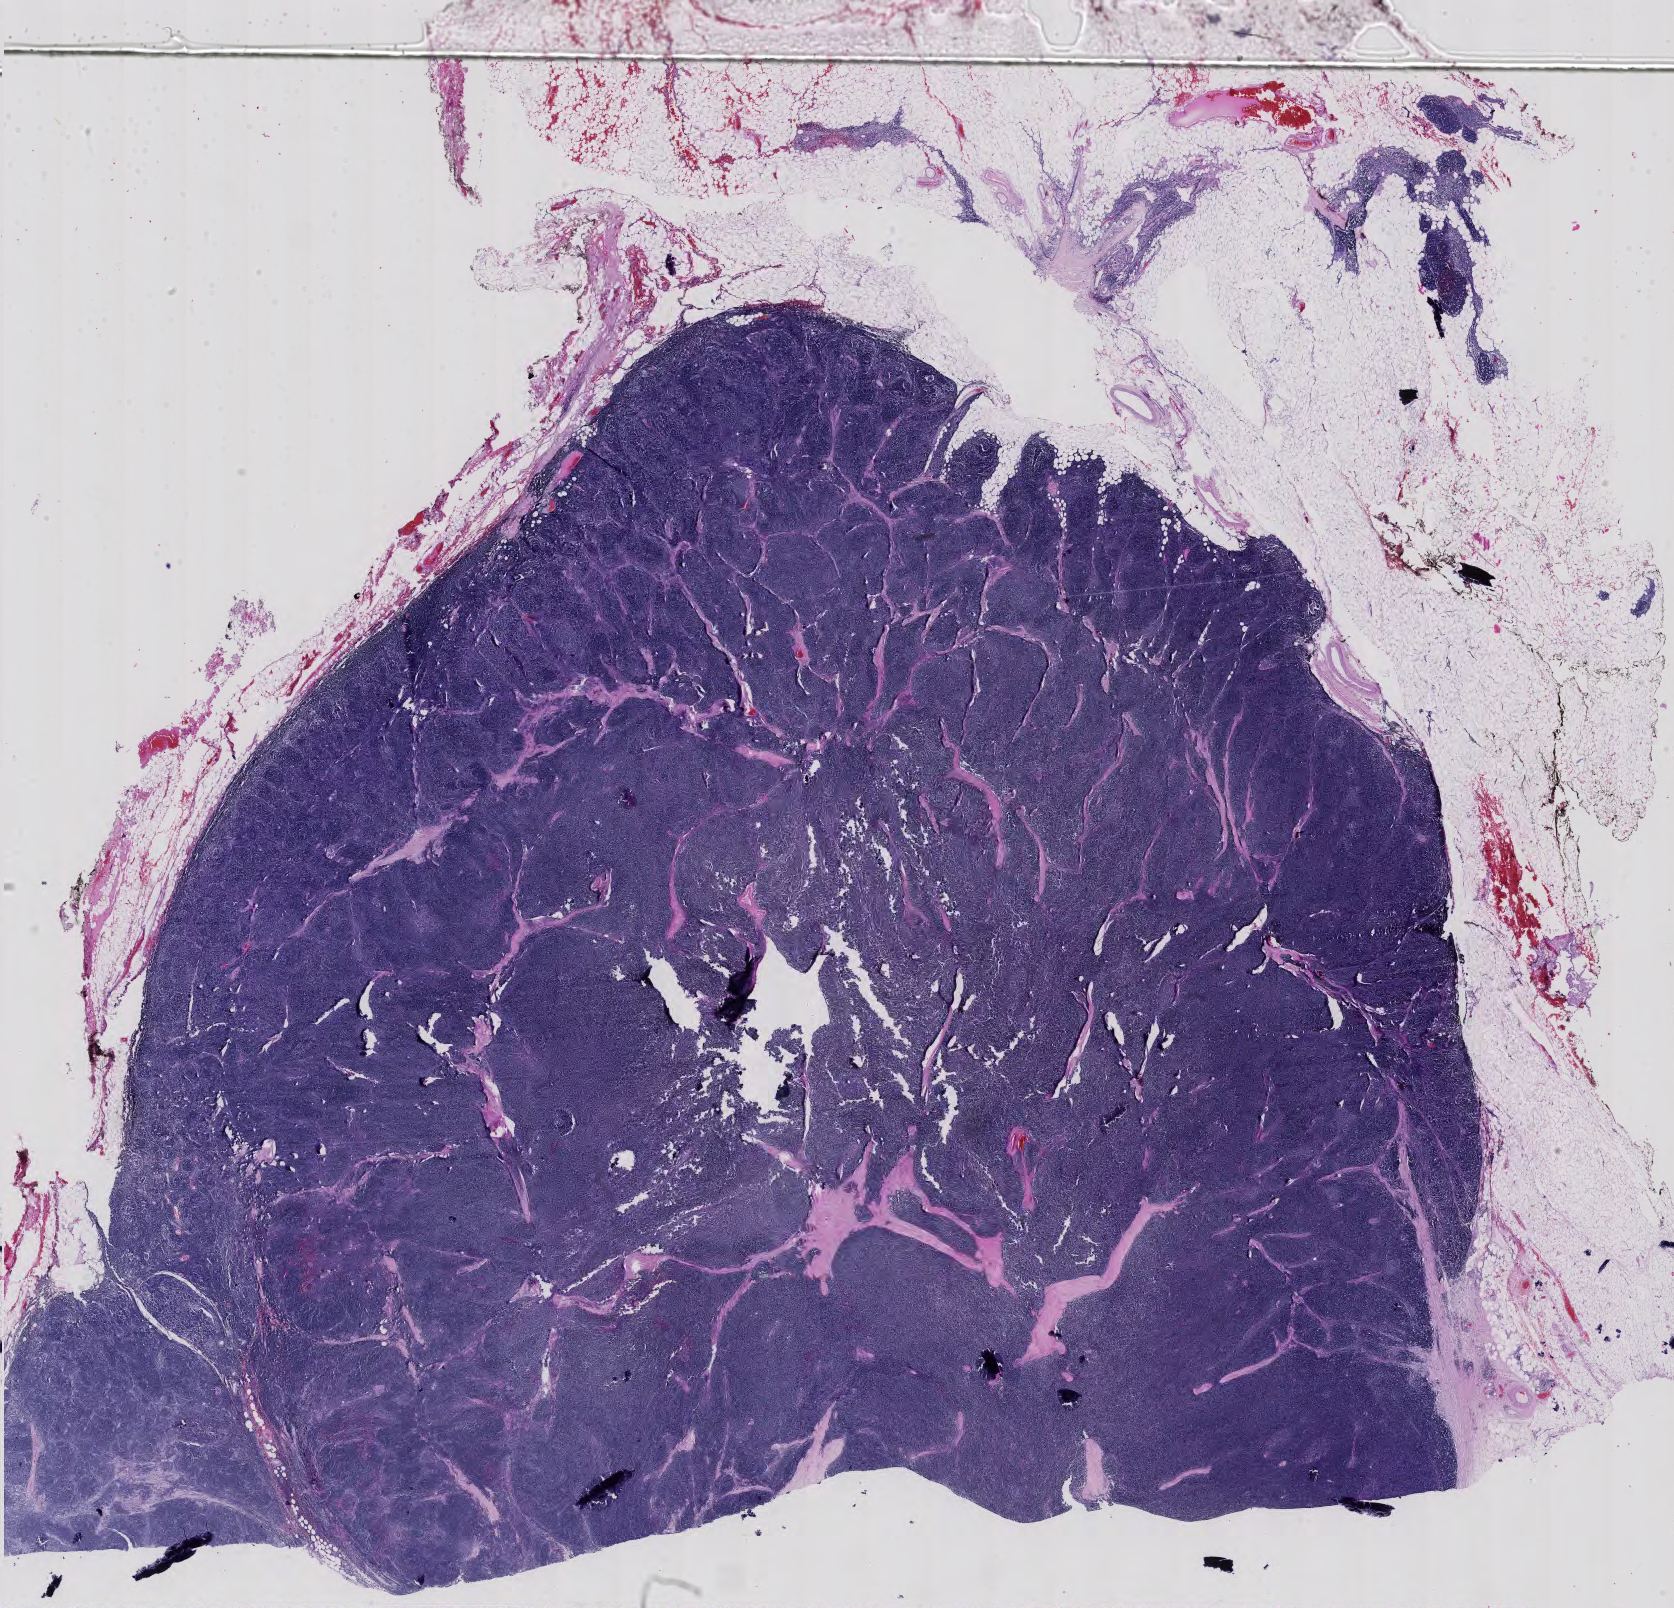
Whole-slide histology image, H&E-stained, a low-resolution overview of the entire scanned area, about 24.4 x 23.5 mm (acquisition: 40x scan). Formalin-fixed paraffin-embedded (FFPE) diagnostic section. Primary tumour sample from the thymus. Female patient; age at initial diagnosis 54 years.
• histologic diagnosis: Thymoma, type B1, malignant (anterior mediastinum)